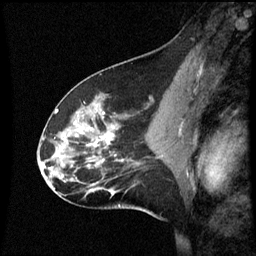
Breast MRI (dynamic contrast-enhanced), one sagittal slice. Position 31 of 60 along the scan axis. Dynamic contrast-enhanced series, image 2 of 3 at this slice position (ordered by acquisition). 1.5 T. TE 4.2 ms, TR 8.9 ms. 2 mm slice thickness. 256 × 256 image matrix, field of view 200 × 200 mm. Female patient, age 45 years. From the clinical record (not read from this slice): setting: breast cancer imaged before/during neoadjuvant chemotherapy; receptor status: HR-positive, HER2-negative.
Structures marked on this image (semi-automatic segmentation, software-assisted and operator-edited):
- analysis volume of interest (the breast-tissue region the enhancement analysis was run in; not a lesion): bounding box <46,94,171,203> (left, top, right, bottom; pixels)
- tumour enhancement mask (voxels above the 70 % enhancement threshold inside the analysis volume of interest): <56,110,123,161>